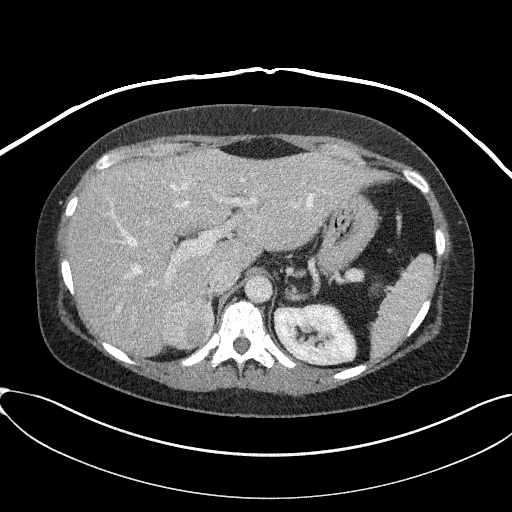
Contrast-enhanced abdominal CT, one axial slice. Position 60 of 95 along the scan axis. 100 kVp. Intravenous contrast given. Soft-tissue window (W 400 / L 40 HU). 3 mm slice thickness. 512 × 512 image matrix, field of view 410 × 410 mm. Patient: female, 46 years. Case-level facts recorded for this patient, not image findings: diagnosis: adrenocortical carcinoma; tumour side: right adrenal; tumour size at pathology: 7.2 cm; Ki-67 index: 50 %.
Structures marked on this image (semi-automatically segmented with operator editing):
- mass: bounding box (x1, y1, x2, y2) in pixels: (164, 295, 213, 347)